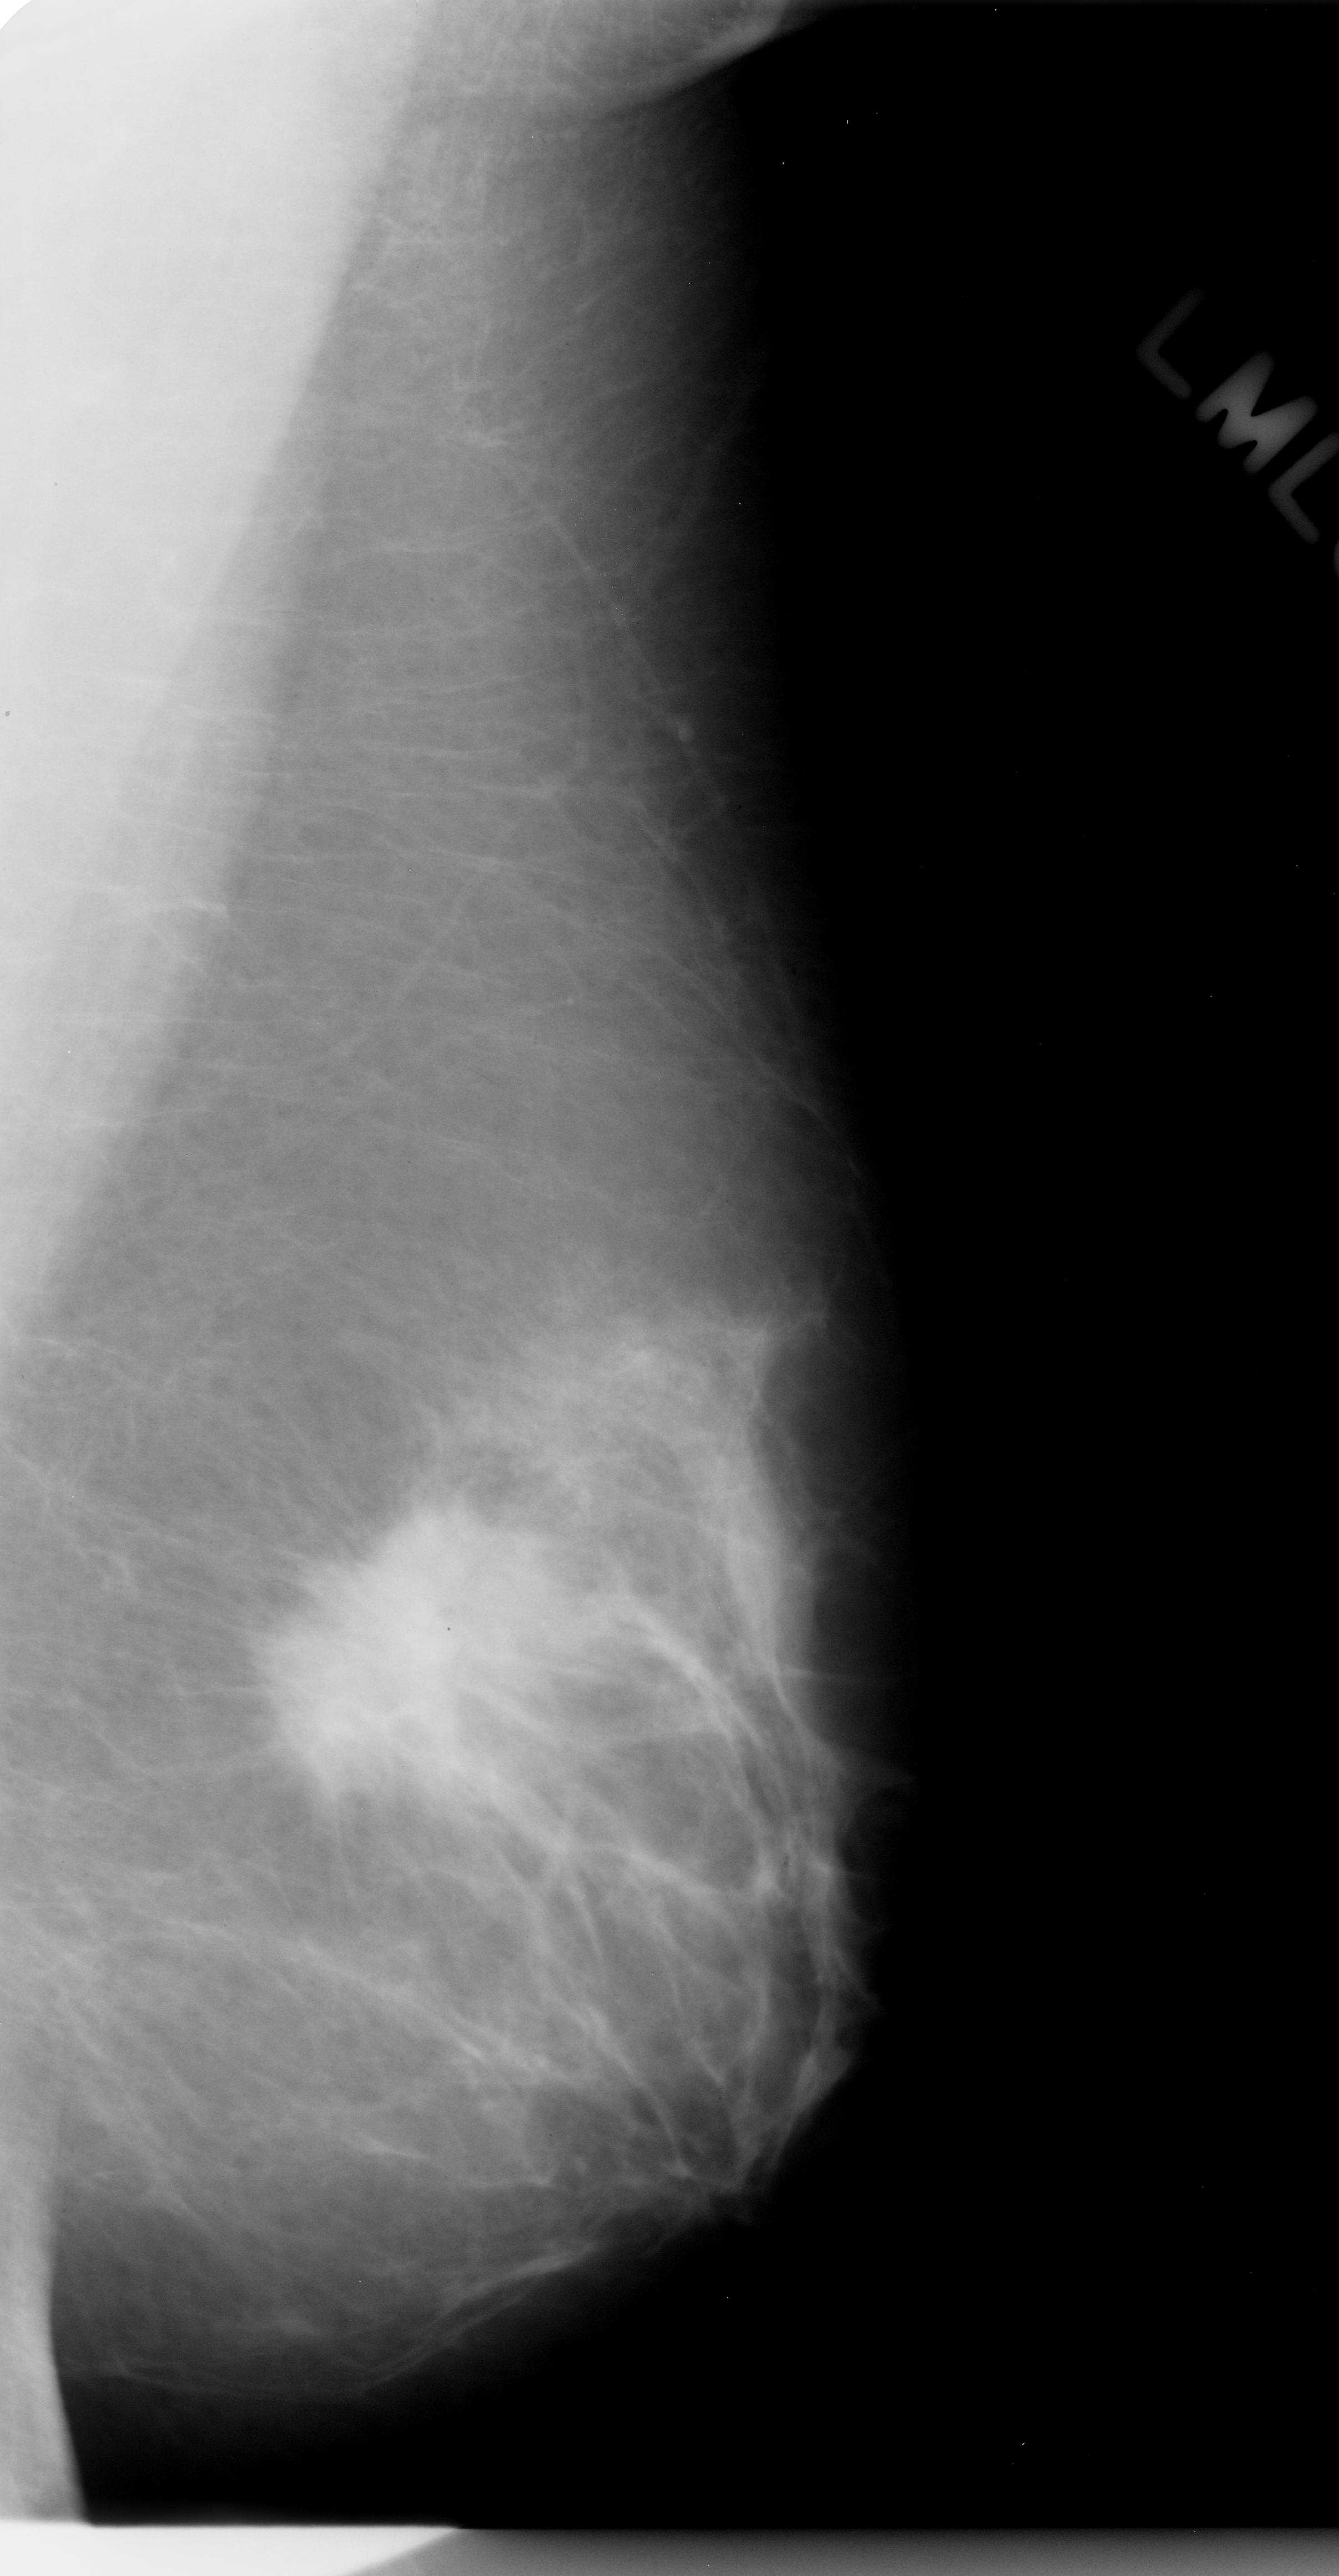
Digitized screen-film mammogram, left breast, mediolateral oblique (MLO) view, BI-RADS breast density category 2 (scale 1–4).
Marked findings (only marked abnormalities are described; nothing is implied about the rest of the image): mass, shape irregular, margins spiculated; BI-RADS assessment category 5; subtlety rating 5 on a 1 (subtle) to 5 (obvious) scale; pathology (as recorded): malignant.